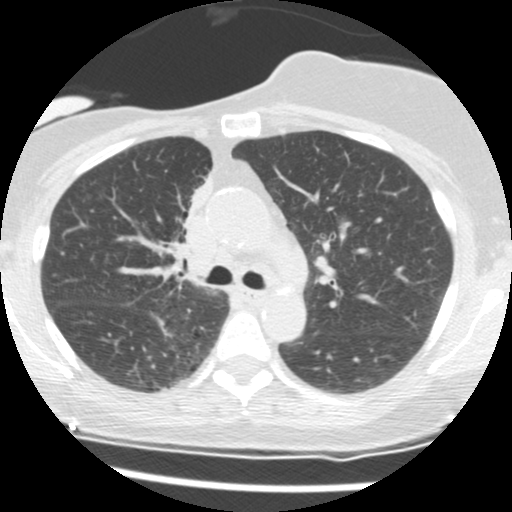
Chest CT (low-dose screening protocol), one axial image, second annual screen, lung window (W 1500 / L -600 HU), 2.5 mm slice thickness, 512 × 512 image matrix, field of view 296 × 296 mm. Female participant, aged 56 years at enrolment. Current smoker at enrolment.
Lesion marked by an expert reader, bounding box (x1, y1, x2, y2) in pixels: (153, 179, 210, 266). The screening reader recorded 2 non-calcified nodules or masses ≥4 mm on this exam (right middle lobe, right lower lobe); which of them this box marks is not recorded. Lung cancer was diagnosed 675 days after this screen (after the third annual screen): adenocarcinoma, NOS, right upper lobe, stage IIIB (AJCC 6th edition), 8 mm at pathology.